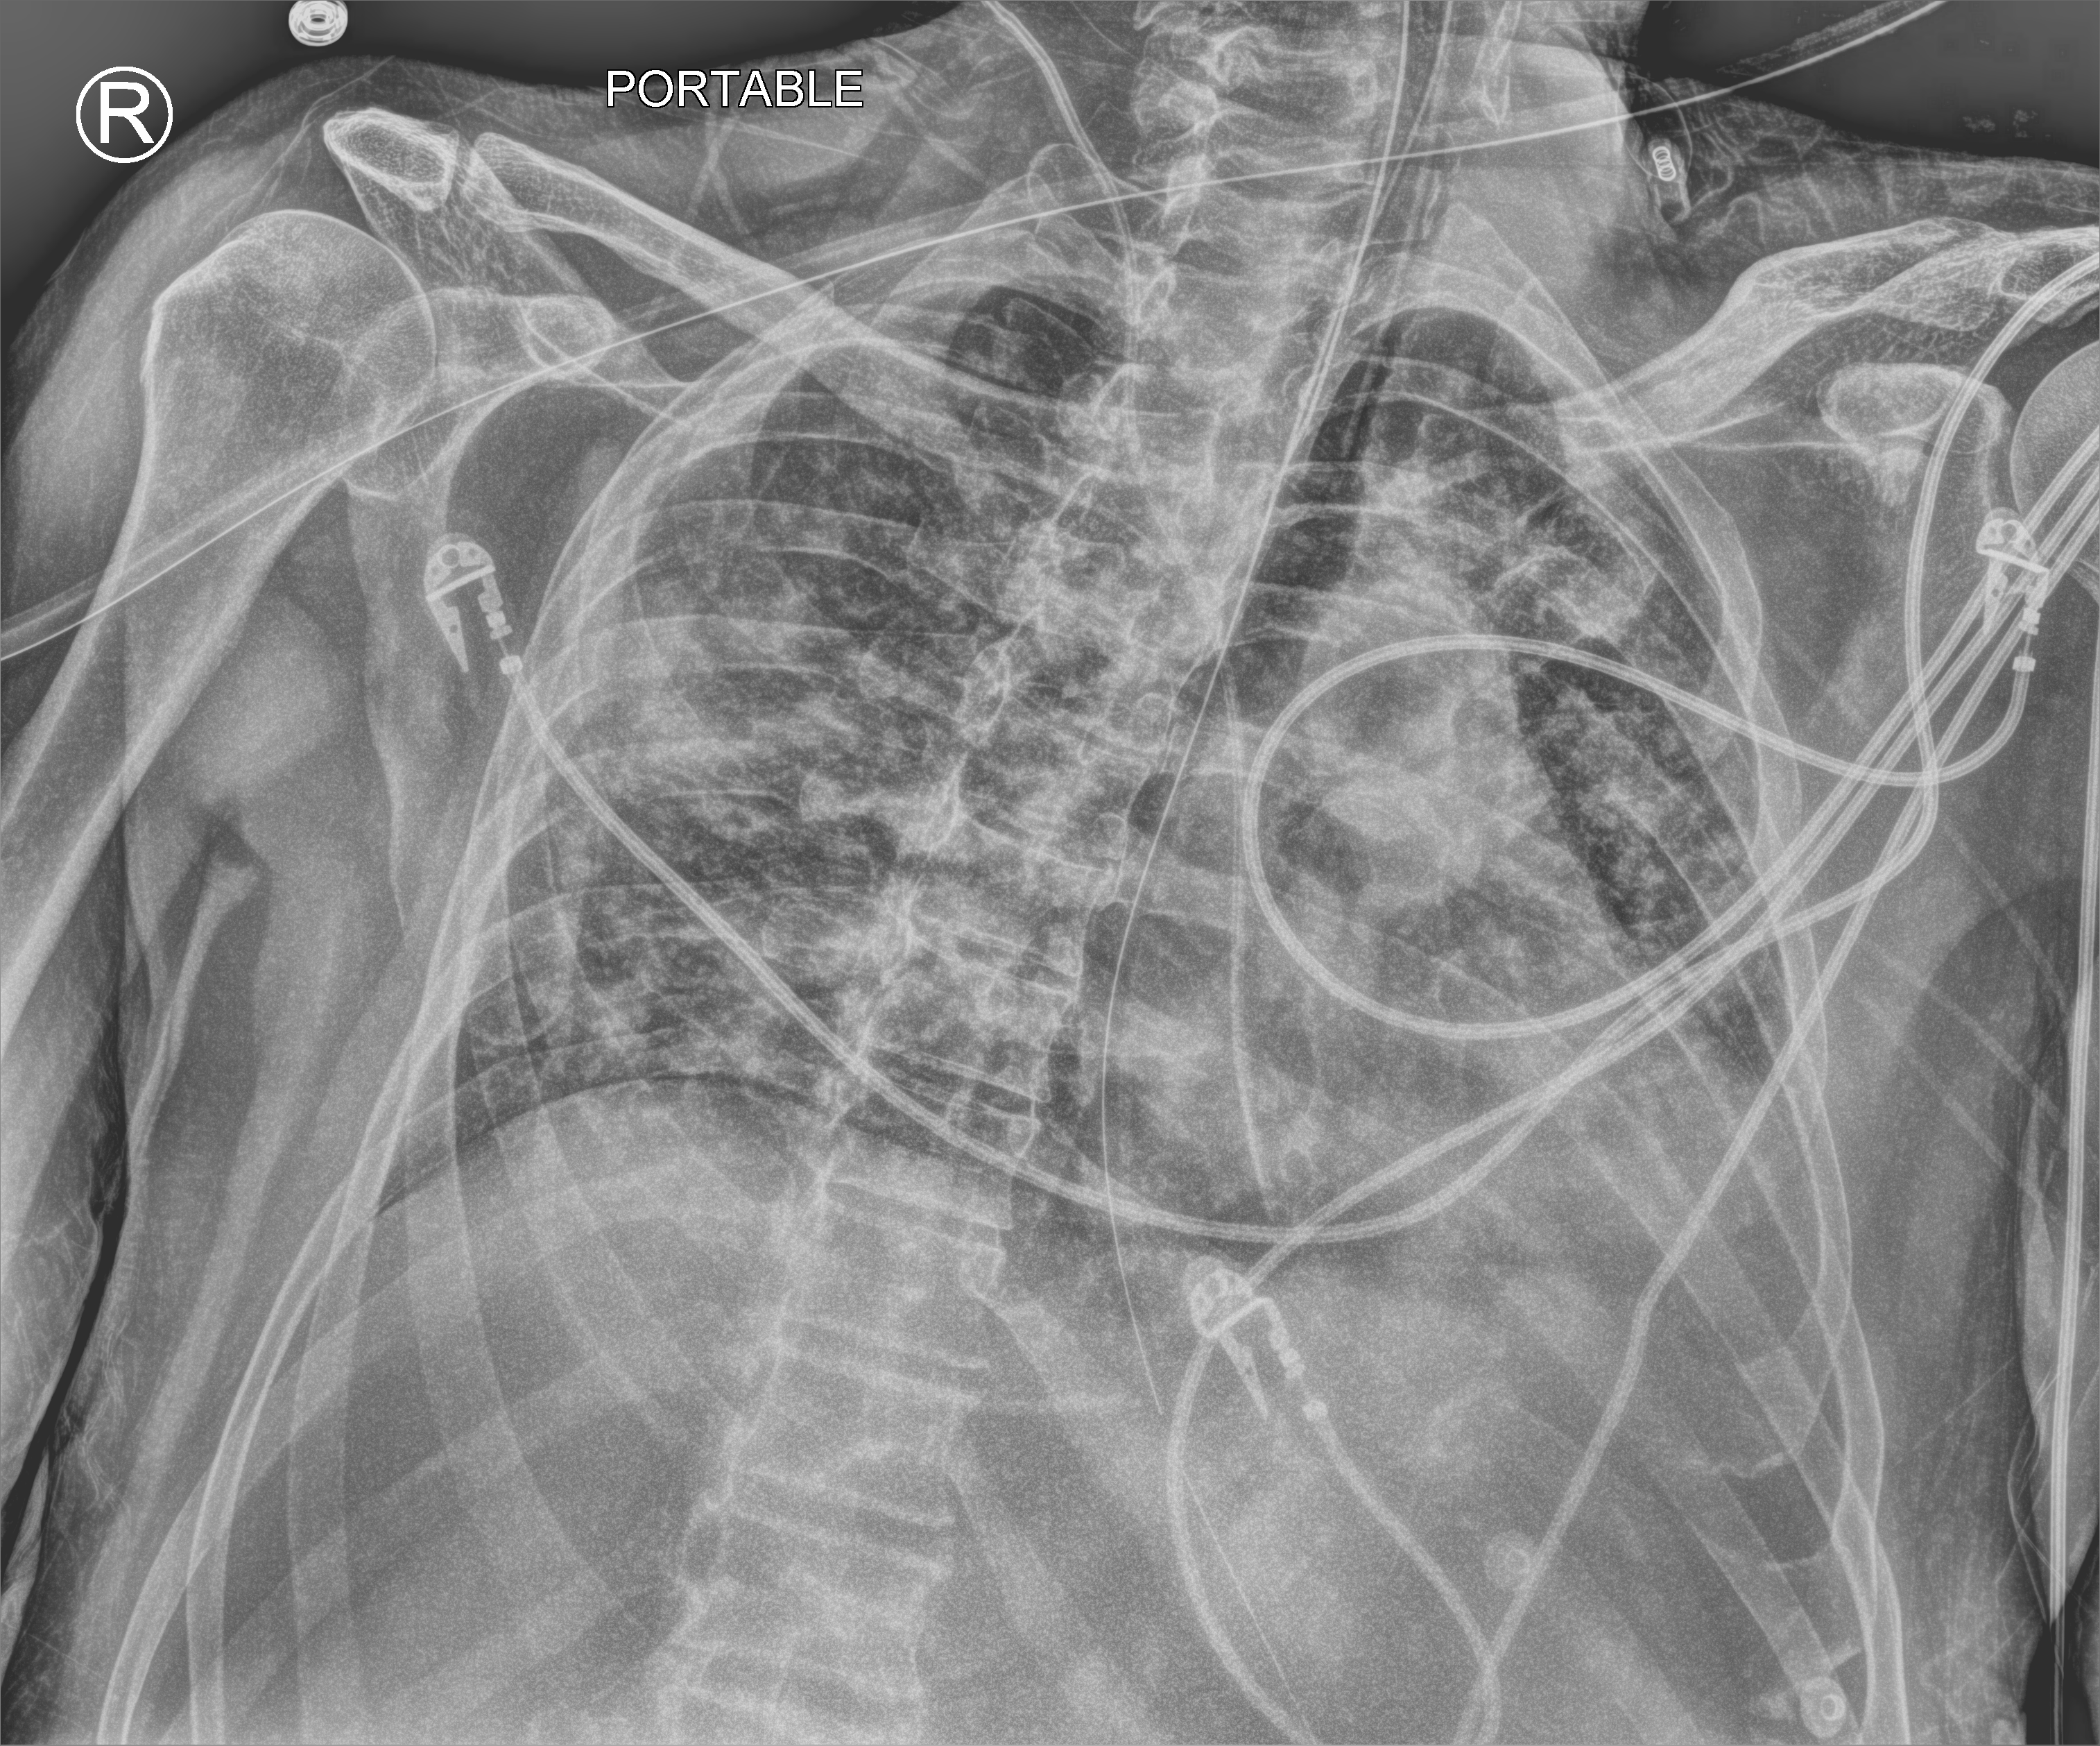
Portable chest radiograph; anteroposterior (AP) projection. Male patient hospitalised with COVID-19, age 18–59 years.
From the hospital-stay record, not from the radiograph (when in the stay this image was taken is not recorded): admitted to intensive care during this hospital stay: yes; mechanically ventilated during this hospital stay: yes.